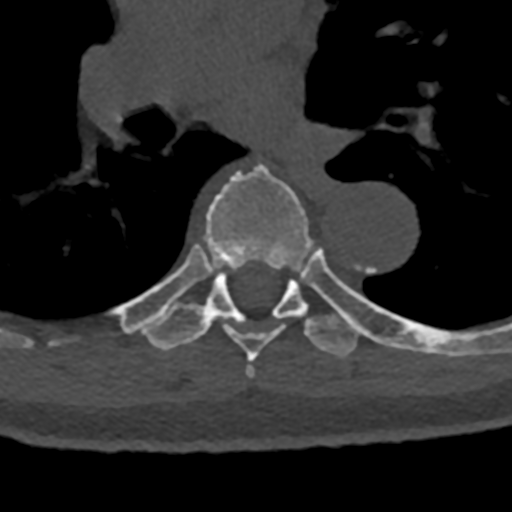
CT including the spine, one axial slice. Reconstruction kernel Br40s/3. 120 kVp. Bone window (W 1800 / L 400 HU). 0.5 mm slice thickness. 512 × 512 image matrix. Male patient, age 74 years. Case-level facts recorded for this patient, not image findings: primary cancer: renal; vertebrae with lytic lesions (as recorded): T10, L1, L2, L3, L4, L5.
Annotated regions visible in this slice (semi-automatically segmented with operator editing):
- T6 vertebra: bounding box (x1, y1, x2, y2) in pixels: (164, 163, 313, 378)
- T7 vertebra: (114, 247, 432, 358)